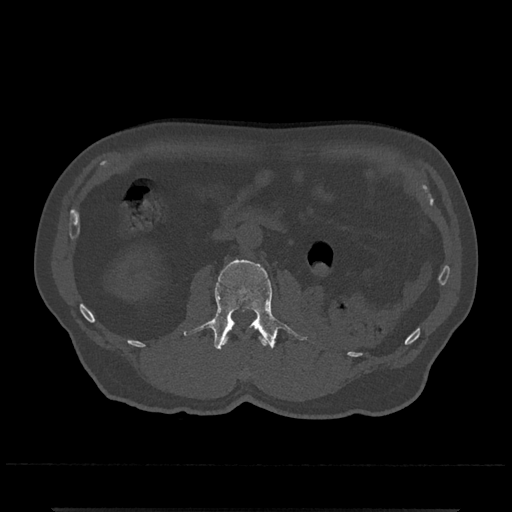
CT including the spine, one axial slice. Position 302 of 797 along the scan axis. Bone window (W 1800 / L 400 HU). 0.5 mm slice thickness. 512 × 512 image matrix, field of view 393 × 393 mm. Male patient, age 67 years. From the clinical record (not read from this slice): primary cancer: prostate.
Annotated regions visible in this slice (semi-automatically segmented with operator editing):
- L1 vertebra: bounding box <223,337,267,347> (left, top, right, bottom; pixels)
- L2 vertebra: <183,259,307,350>